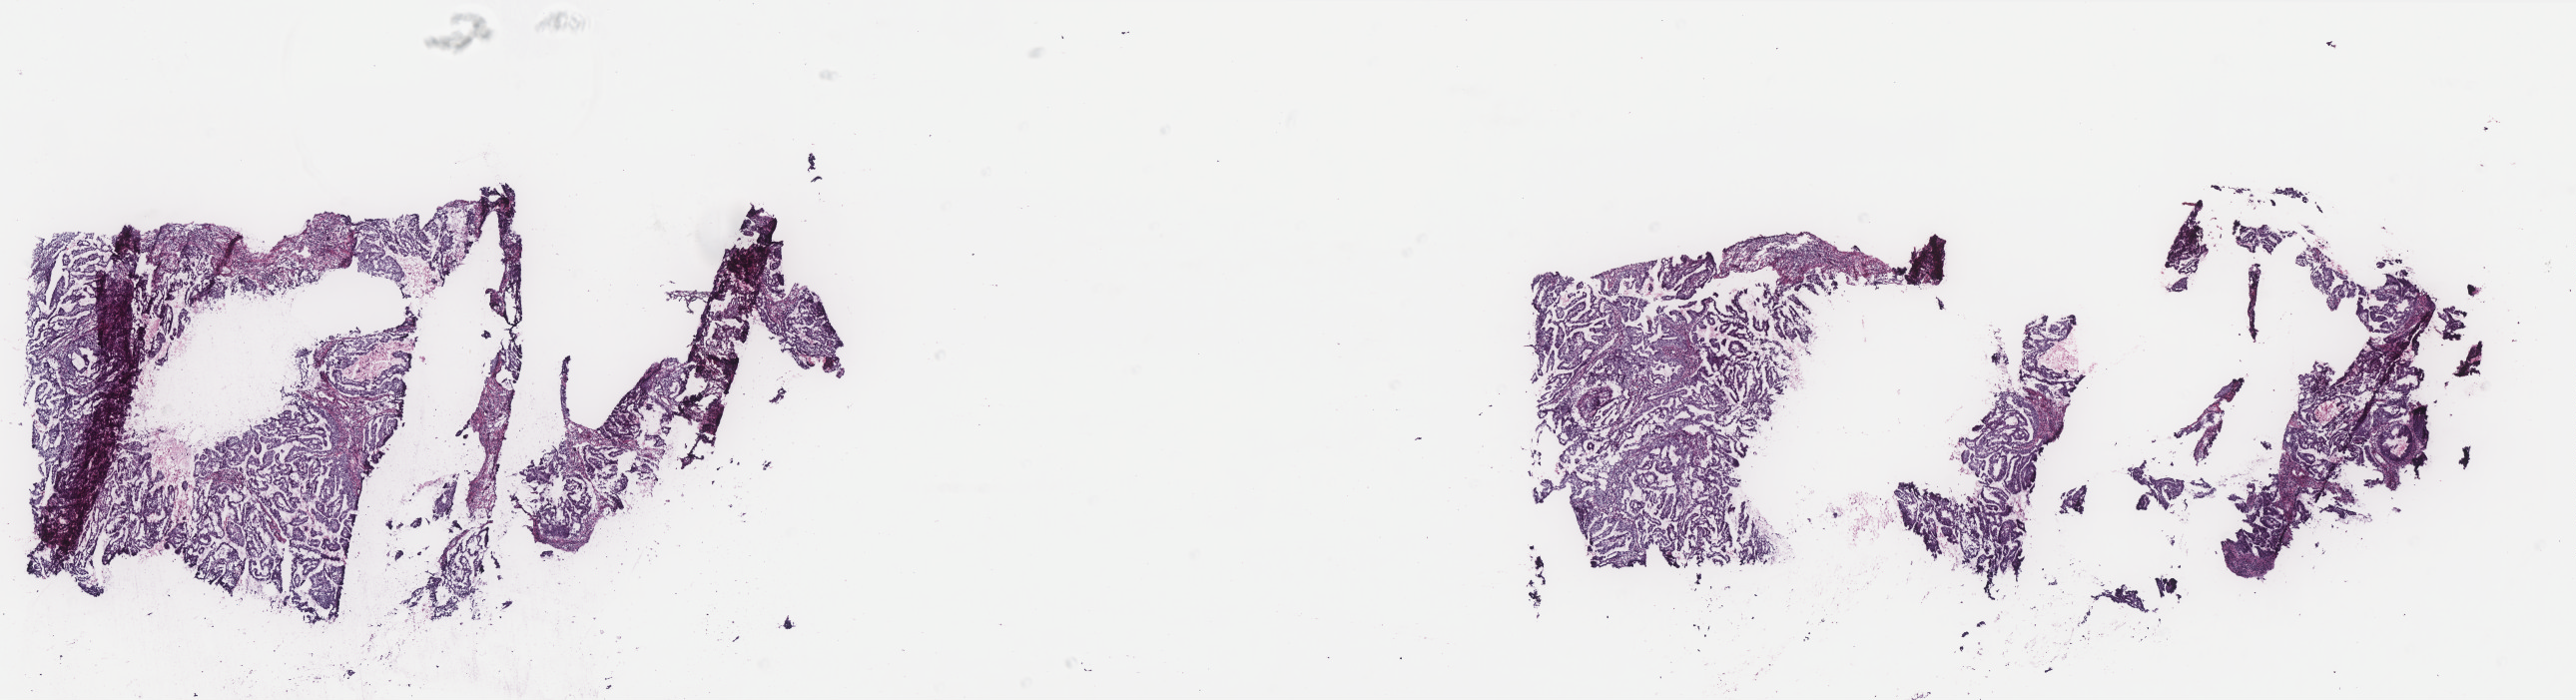
H&E-stained whole-slide image — shown as a low-resolution overview of the whole scanned area (about 20.7 x 5.6 mm); frozen section from the bottom of the tissue portion; primary tumour sample from the uterus. Female patient; age at initial diagnosis 37 years. Histologic grade: G1 (well differentiated). Composition of this section per pathologist review: tumour cells 60%, tumour nuclei 80%, normal cells 0%, stromal cells 20%, necrosis 20%. Inflammatory infiltration, as recorded: lymphocyte infiltration 20%, monocyte infiltration 0%, neutrophil infiltration 10%.
* pathologic diagnosis: Endometrioid adenocarcinoma, NOS (endometrium)
* FIGO stage: IA